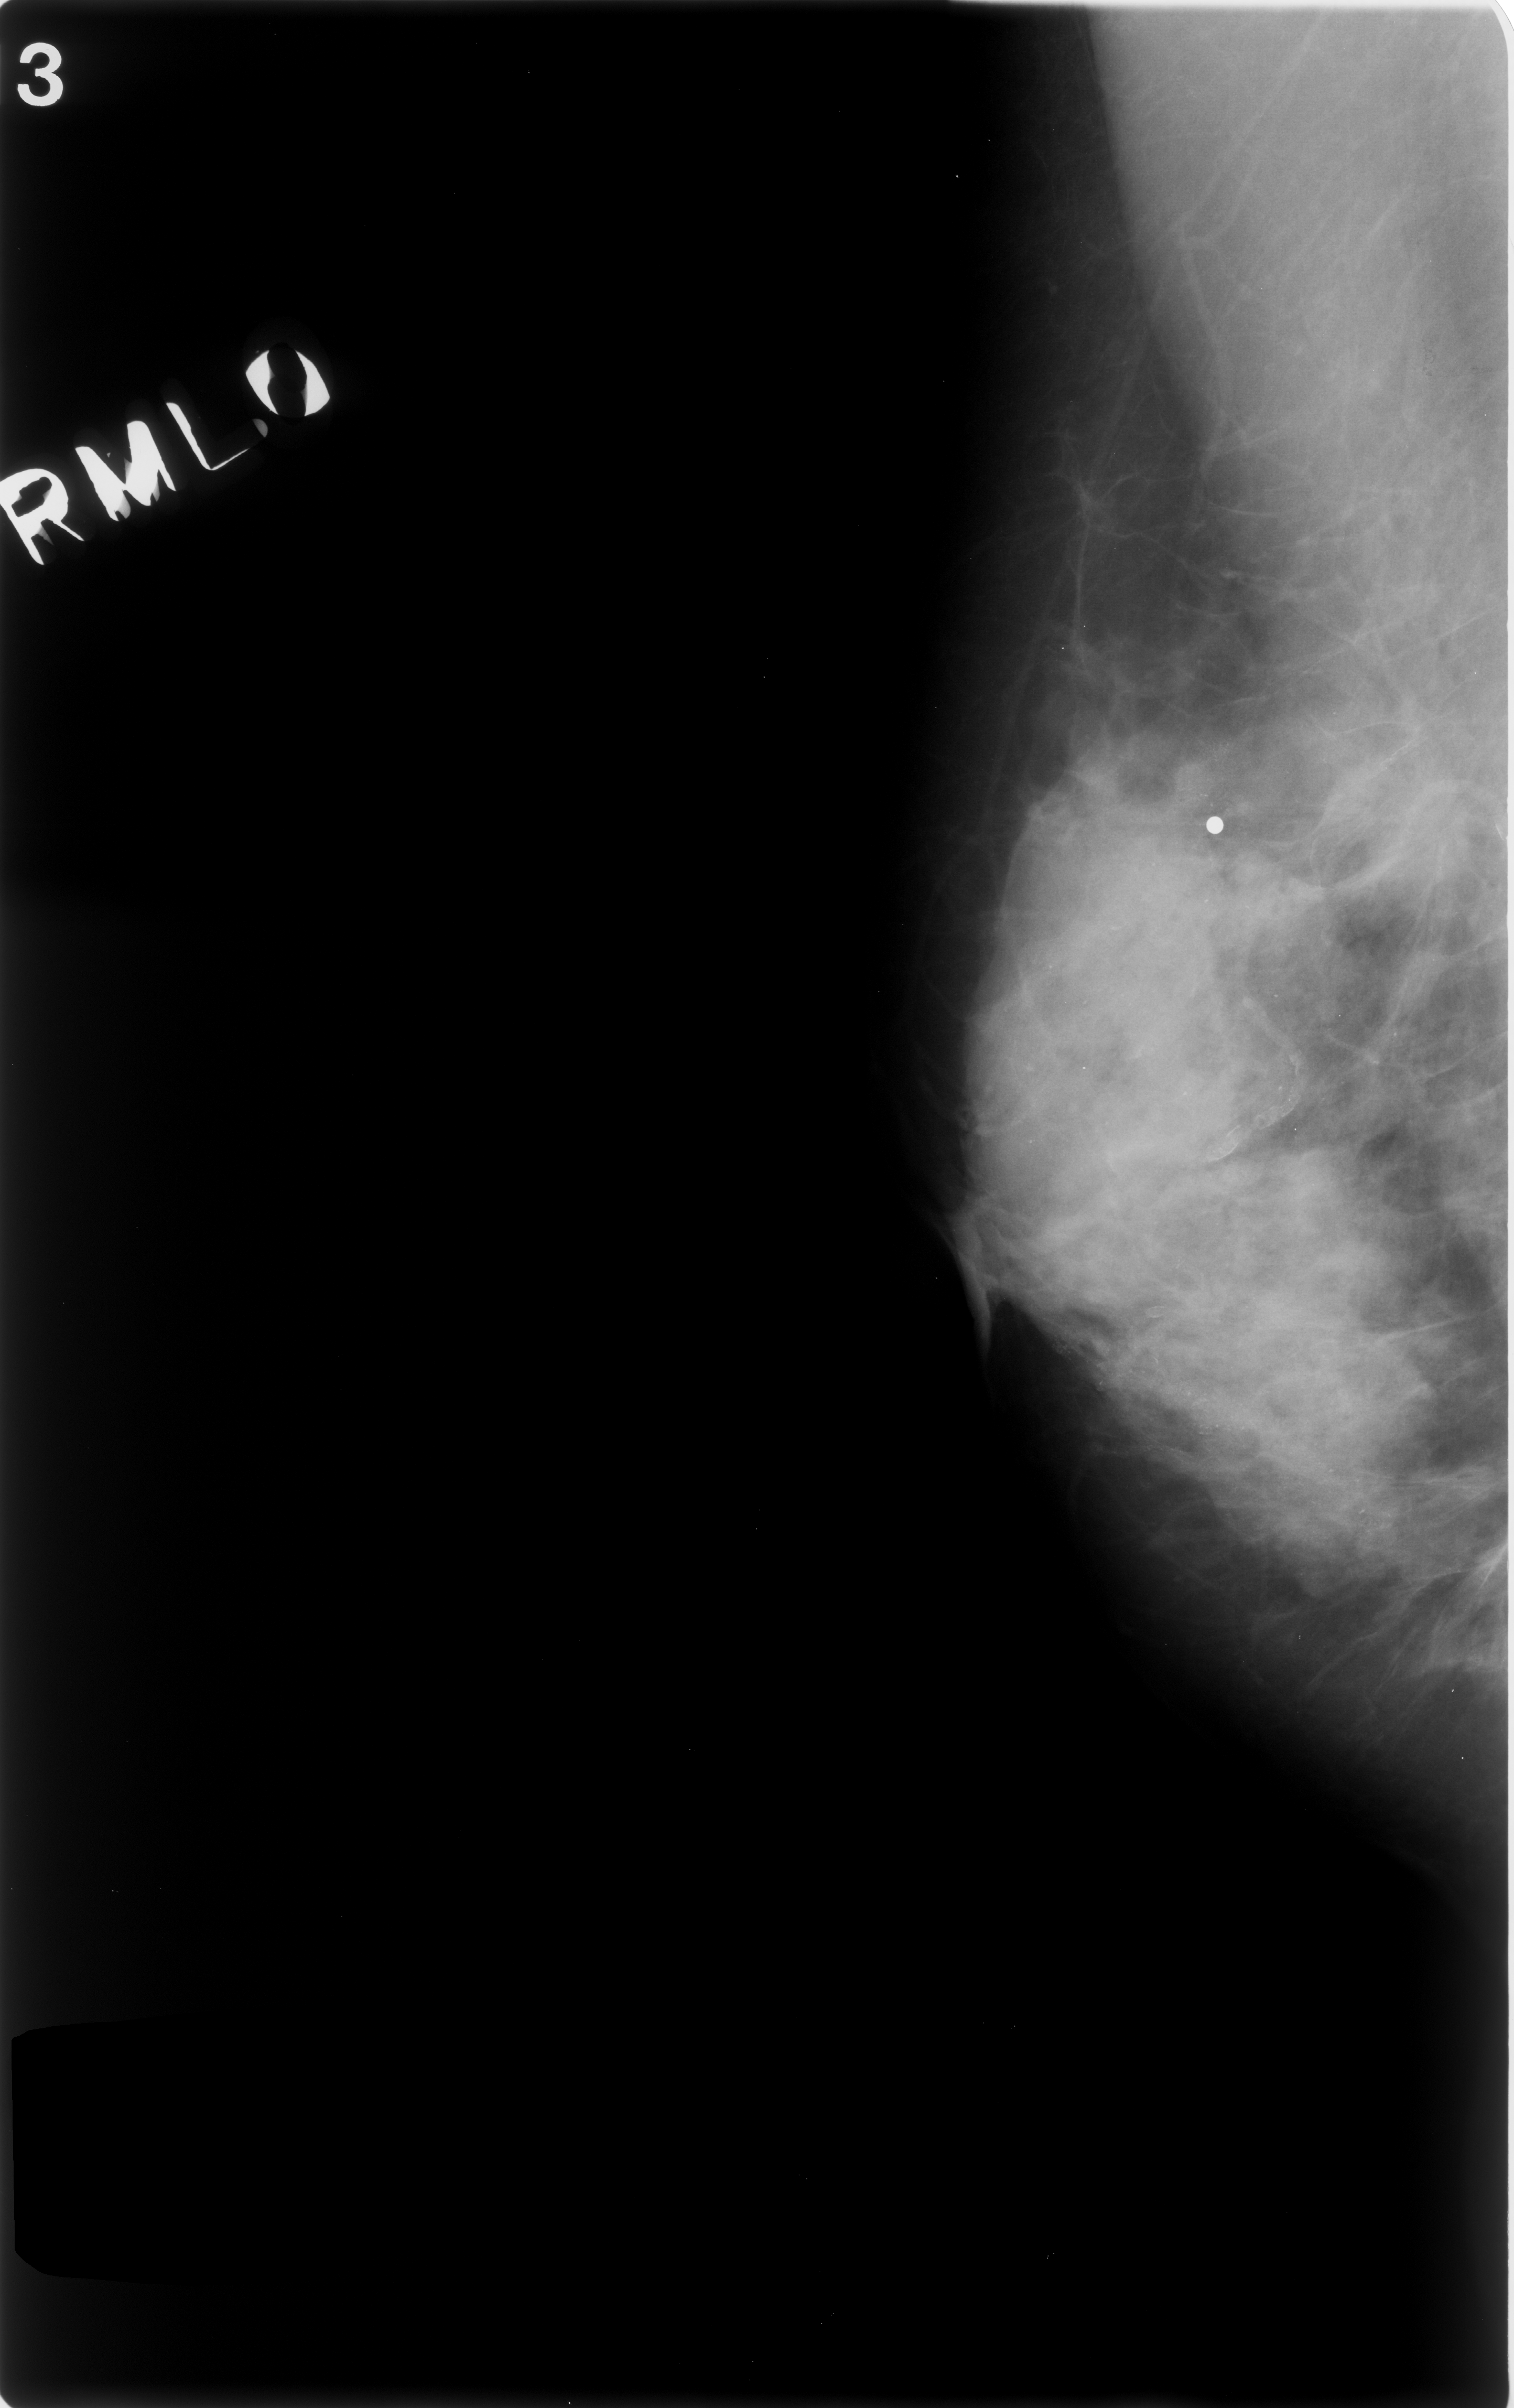
Mammogram (digitized film); right breast; MLO view; breast composition: extremely dense (BI-RADS density category 4 of 4); 1514 × 2408 image matrix.
Marked abnormalities (boxes around the expert regions of interest):
- mass, shape architectural distortion, margins spiculated; BI-RADS assessment category 5; subtlety rating 3 on a 1 (subtle) to 5 (obvious) scale; pathology (as recorded): malignant: bounding box <1309,676,1462,914> (left, top, right, bottom; pixels)